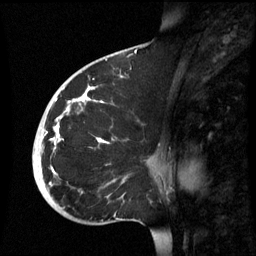
Breast MRI (dynamic contrast-enhanced), one sagittal slice. Position 34 of 60 along the scan axis. Dynamic contrast-enhanced series, image 2 of 3 at this slice position (ordered by acquisition). 1.5 T. TE 4.2 ms, TR 8.9 ms. 2.6 mm slice thickness. 256 × 256 image matrix, field of view 220 × 220 mm. Patient: female, 35 years. From the clinical record (not read from this slice): setting: breast cancer imaged before/during neoadjuvant chemotherapy; receptor status: HR-positive, HER2-negative.
Outlined on this slice (semi-automatic segmentation, software-assisted and operator-edited):
- analysis volume of interest (the breast-tissue region the enhancement analysis was run in; not a lesion): bounding box [x1, y1, x2, y2] px = [32, 74, 164, 221]
- tumour enhancement mask (voxels above the 70 % enhancement threshold inside the analysis volume of interest): [39, 88, 107, 185]